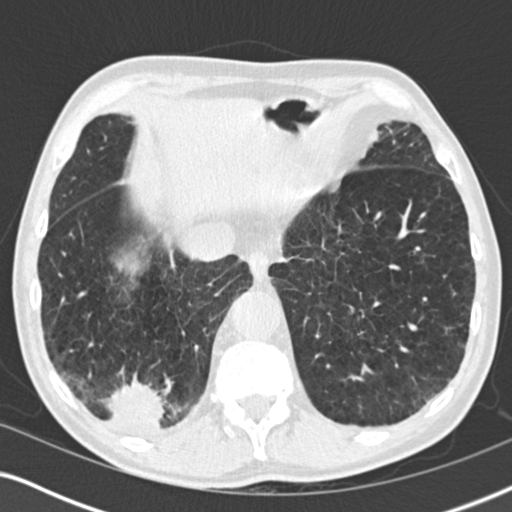
Low-dose screening chest CT, one axial slice. Position 54 of 196 along the scan axis. Lung window (W 1500 / L -600 HU). 2 mm slice thickness. 512 × 512 image matrix, field of view 330 × 330 mm.
Annotated regions visible in this slice (manually delineated by an expert):
- lesion 3 (tumor, lower lobe of right lung): bounding box [x1, y1, x2, y2] px = [104, 381, 166, 430]